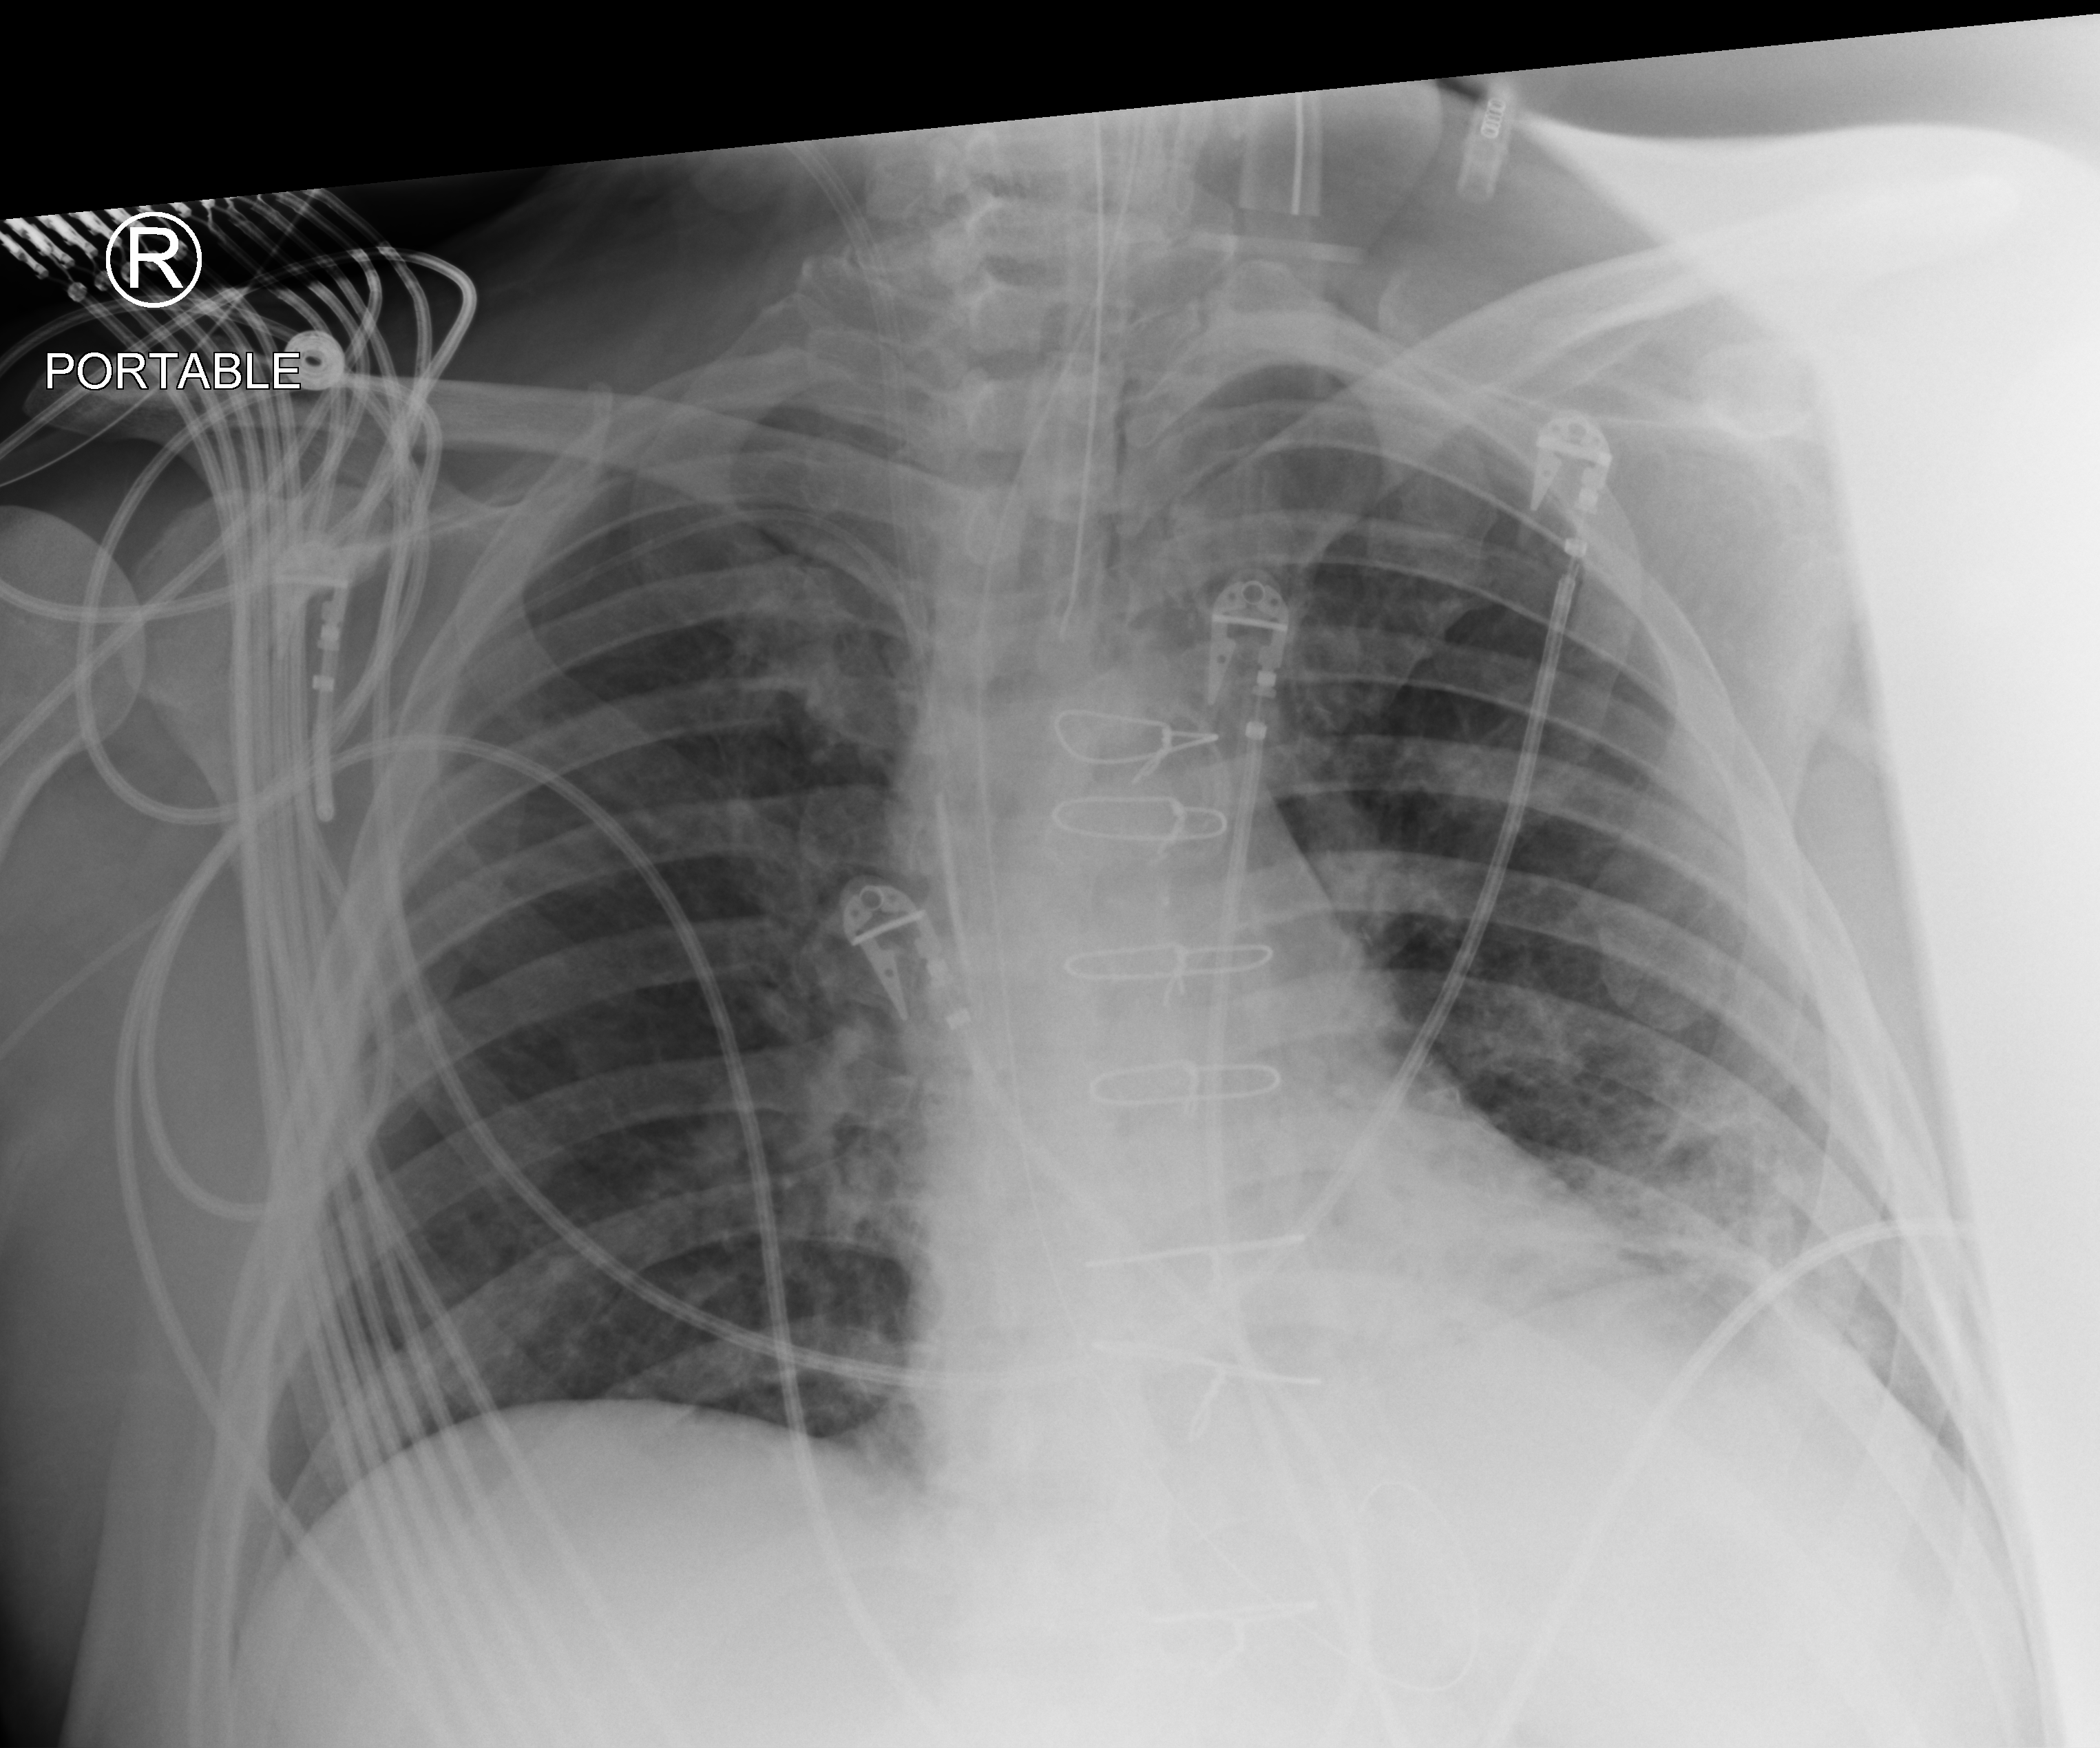
Portable chest radiograph; anteroposterior (AP) projection. Patient hospitalised with COVID-19; male, aged 60–74 years.
Admission-level facts for this patient (not findings on this image; timing relative to this image not recorded): mechanically ventilated during this hospital stay: yes; chronic kidney disease (admission record): no.